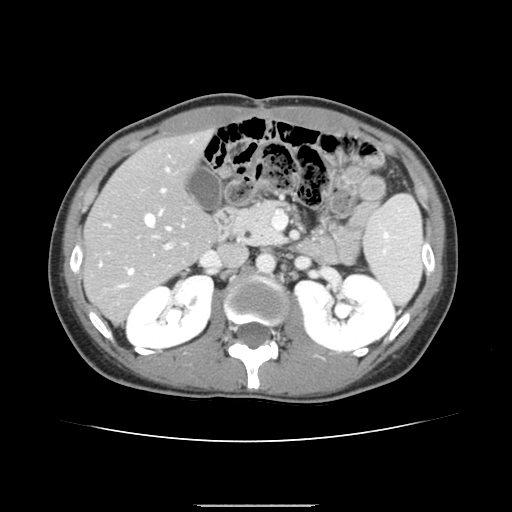
Contrast-enhanced abdominal CT, one axial slice; slice 78 of 150 in the series (ordered by position); intravenous contrast given; soft-tissue window (W 400 / L 40 HU); 2.5 mm slice thickness; 512 × 512 image matrix, field of view 324 × 324 mm. Female patient, age 32 years. Case-level facts recorded for this patient, not image findings: diagnosis: colorectal cancer liver metastases, imaged before liver resection; multiple liver metastases: yes.
Outlined on this slice (expert manual segmentation):
- hepatic veins: bounding box (x1, y1, x2, y2) in pixels: (100, 211, 170, 274)
- liver: (85, 133, 216, 320)
- planned liver remnant (the part of the liver to remain after resection): (86, 132, 215, 278)
- portal vein (with intrahepatic branches): (105, 140, 193, 287)